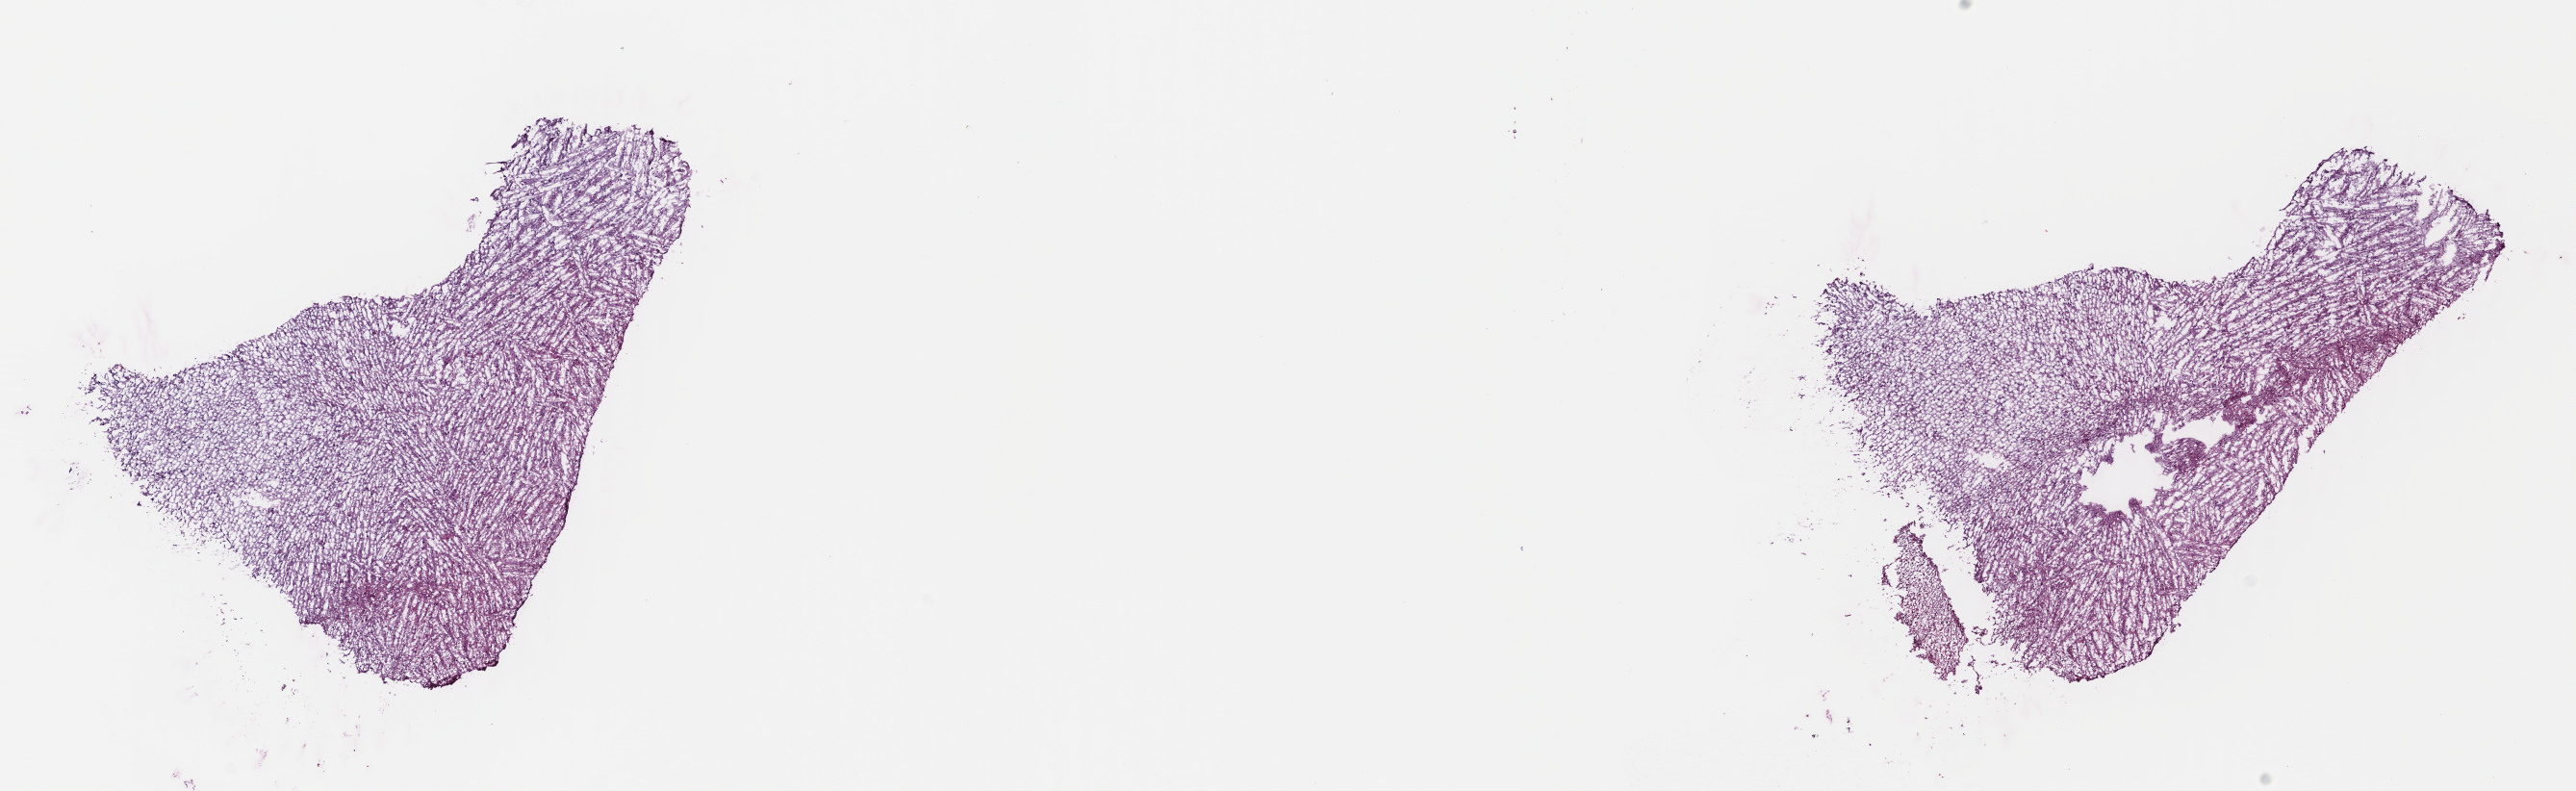
Digitized H&E tissue section (whole slide) — low-resolution overview of the scanned area, about 21.0 x 6.5 mm. Frozen section from the top of the tissue portion. Brain, primary tumour sample. Female patient; age at initial diagnosis 36 years. Pathologist review of this section (percent, as recorded): tumour cells 40%, tumour nuclei 75%.
Diagnosis: Astrocytoma, anaplastic (cerebrum).